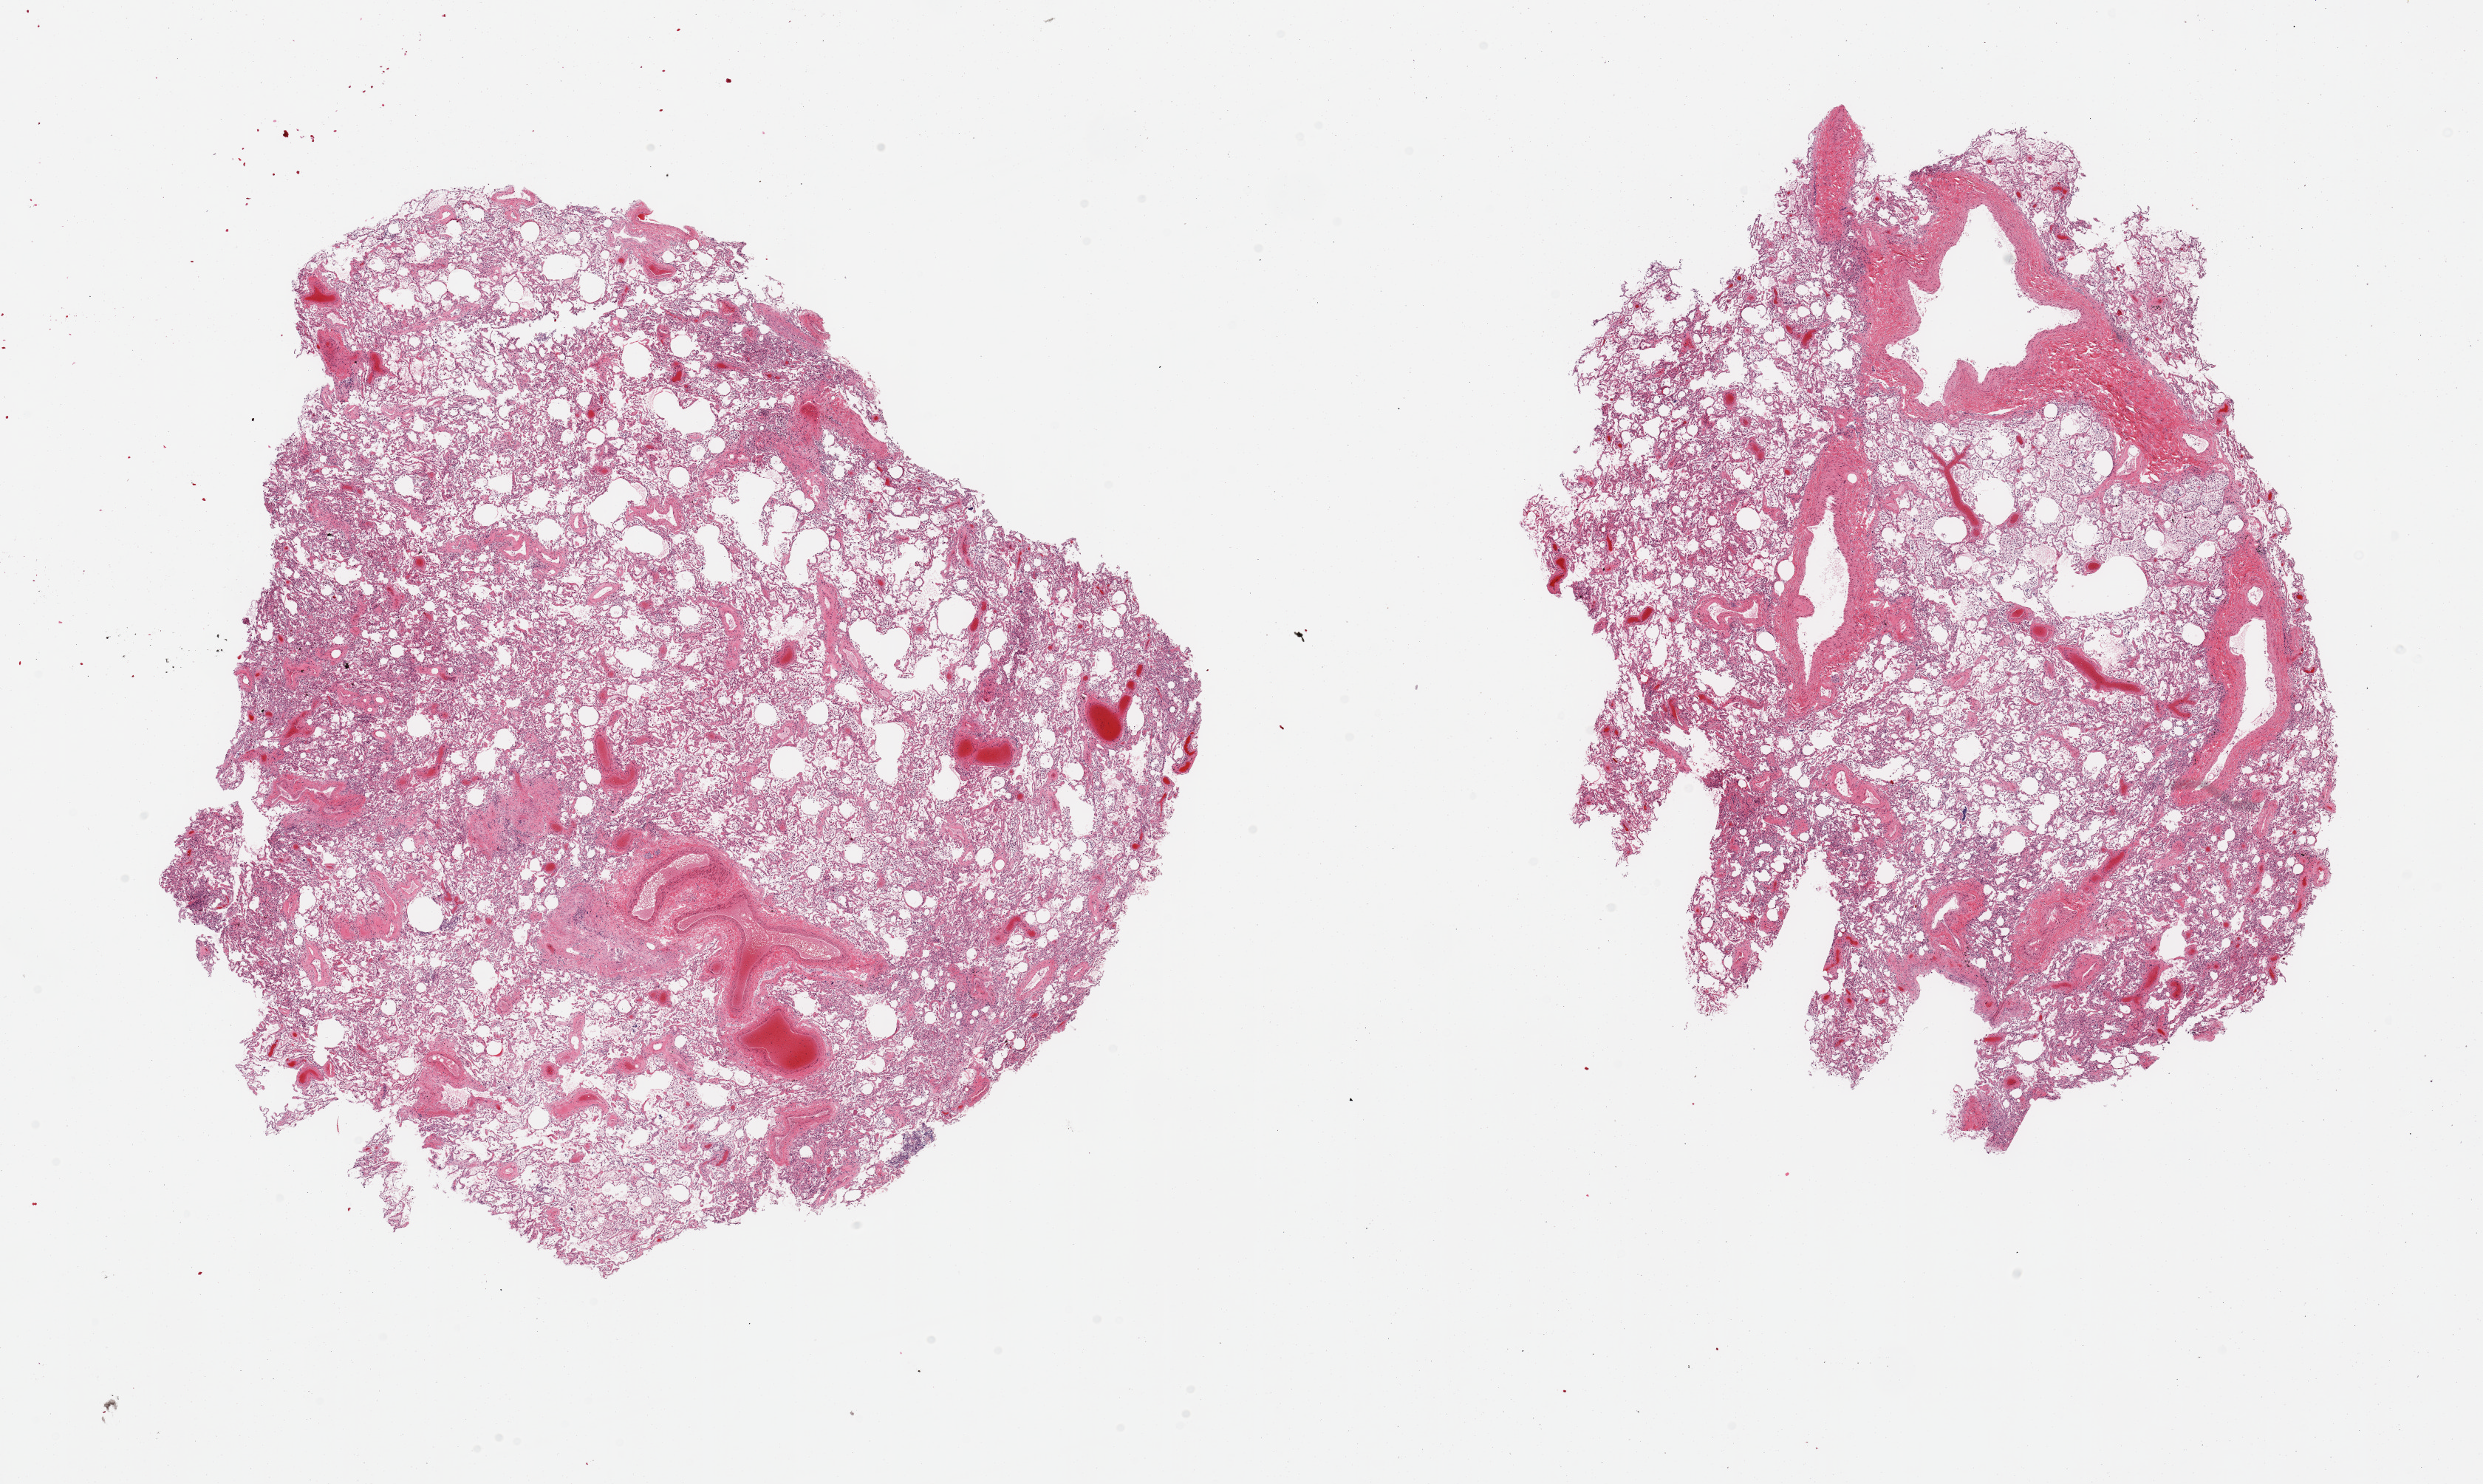
Hematoxylin and eosin (H&E) whole-slide image, a low-resolution overview of the entire scanned area, about 26.6 x 15.9 mm (acquisition: 20x scan). PAXgene-fixed paraffin-embedded (PFPE) section. Sampled site (target tissue): lung. Tissue donor sample. Donor: male.
Pathologist's review note for this sample: 2 pieces.